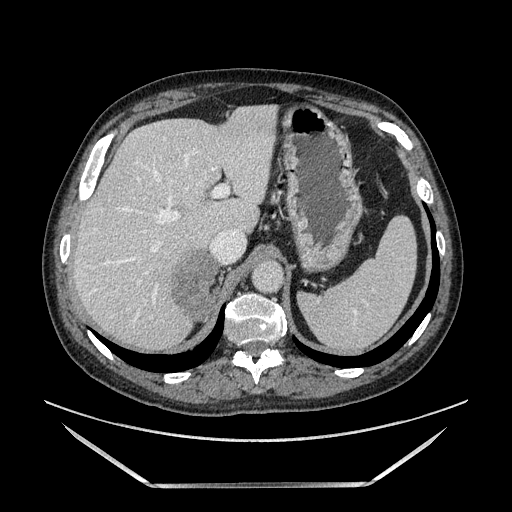
Contrast-enhanced abdominal CT, one axial slice; slice 108 of 185 in the series (ordered by position); soft-tissue window (W 400 / L 40 HU); 1.25 mm slice thickness; 512 × 512 image matrix, field of view 440 × 440 mm. Male patient. From the clinical record (not read from this slice): diagnosis: adrenocortical carcinoma; tumour side: right adrenal; tumour size at pathology: 10.3 cm; Ki-67 index: 20 %; stage (as recorded): 3.
Annotated regions visible in this slice (semi-automatic segmentation, software-assisted and operator-edited):
- mass: bounding box (x1, y1, x2, y2) in pixels: (175, 254, 216, 317)